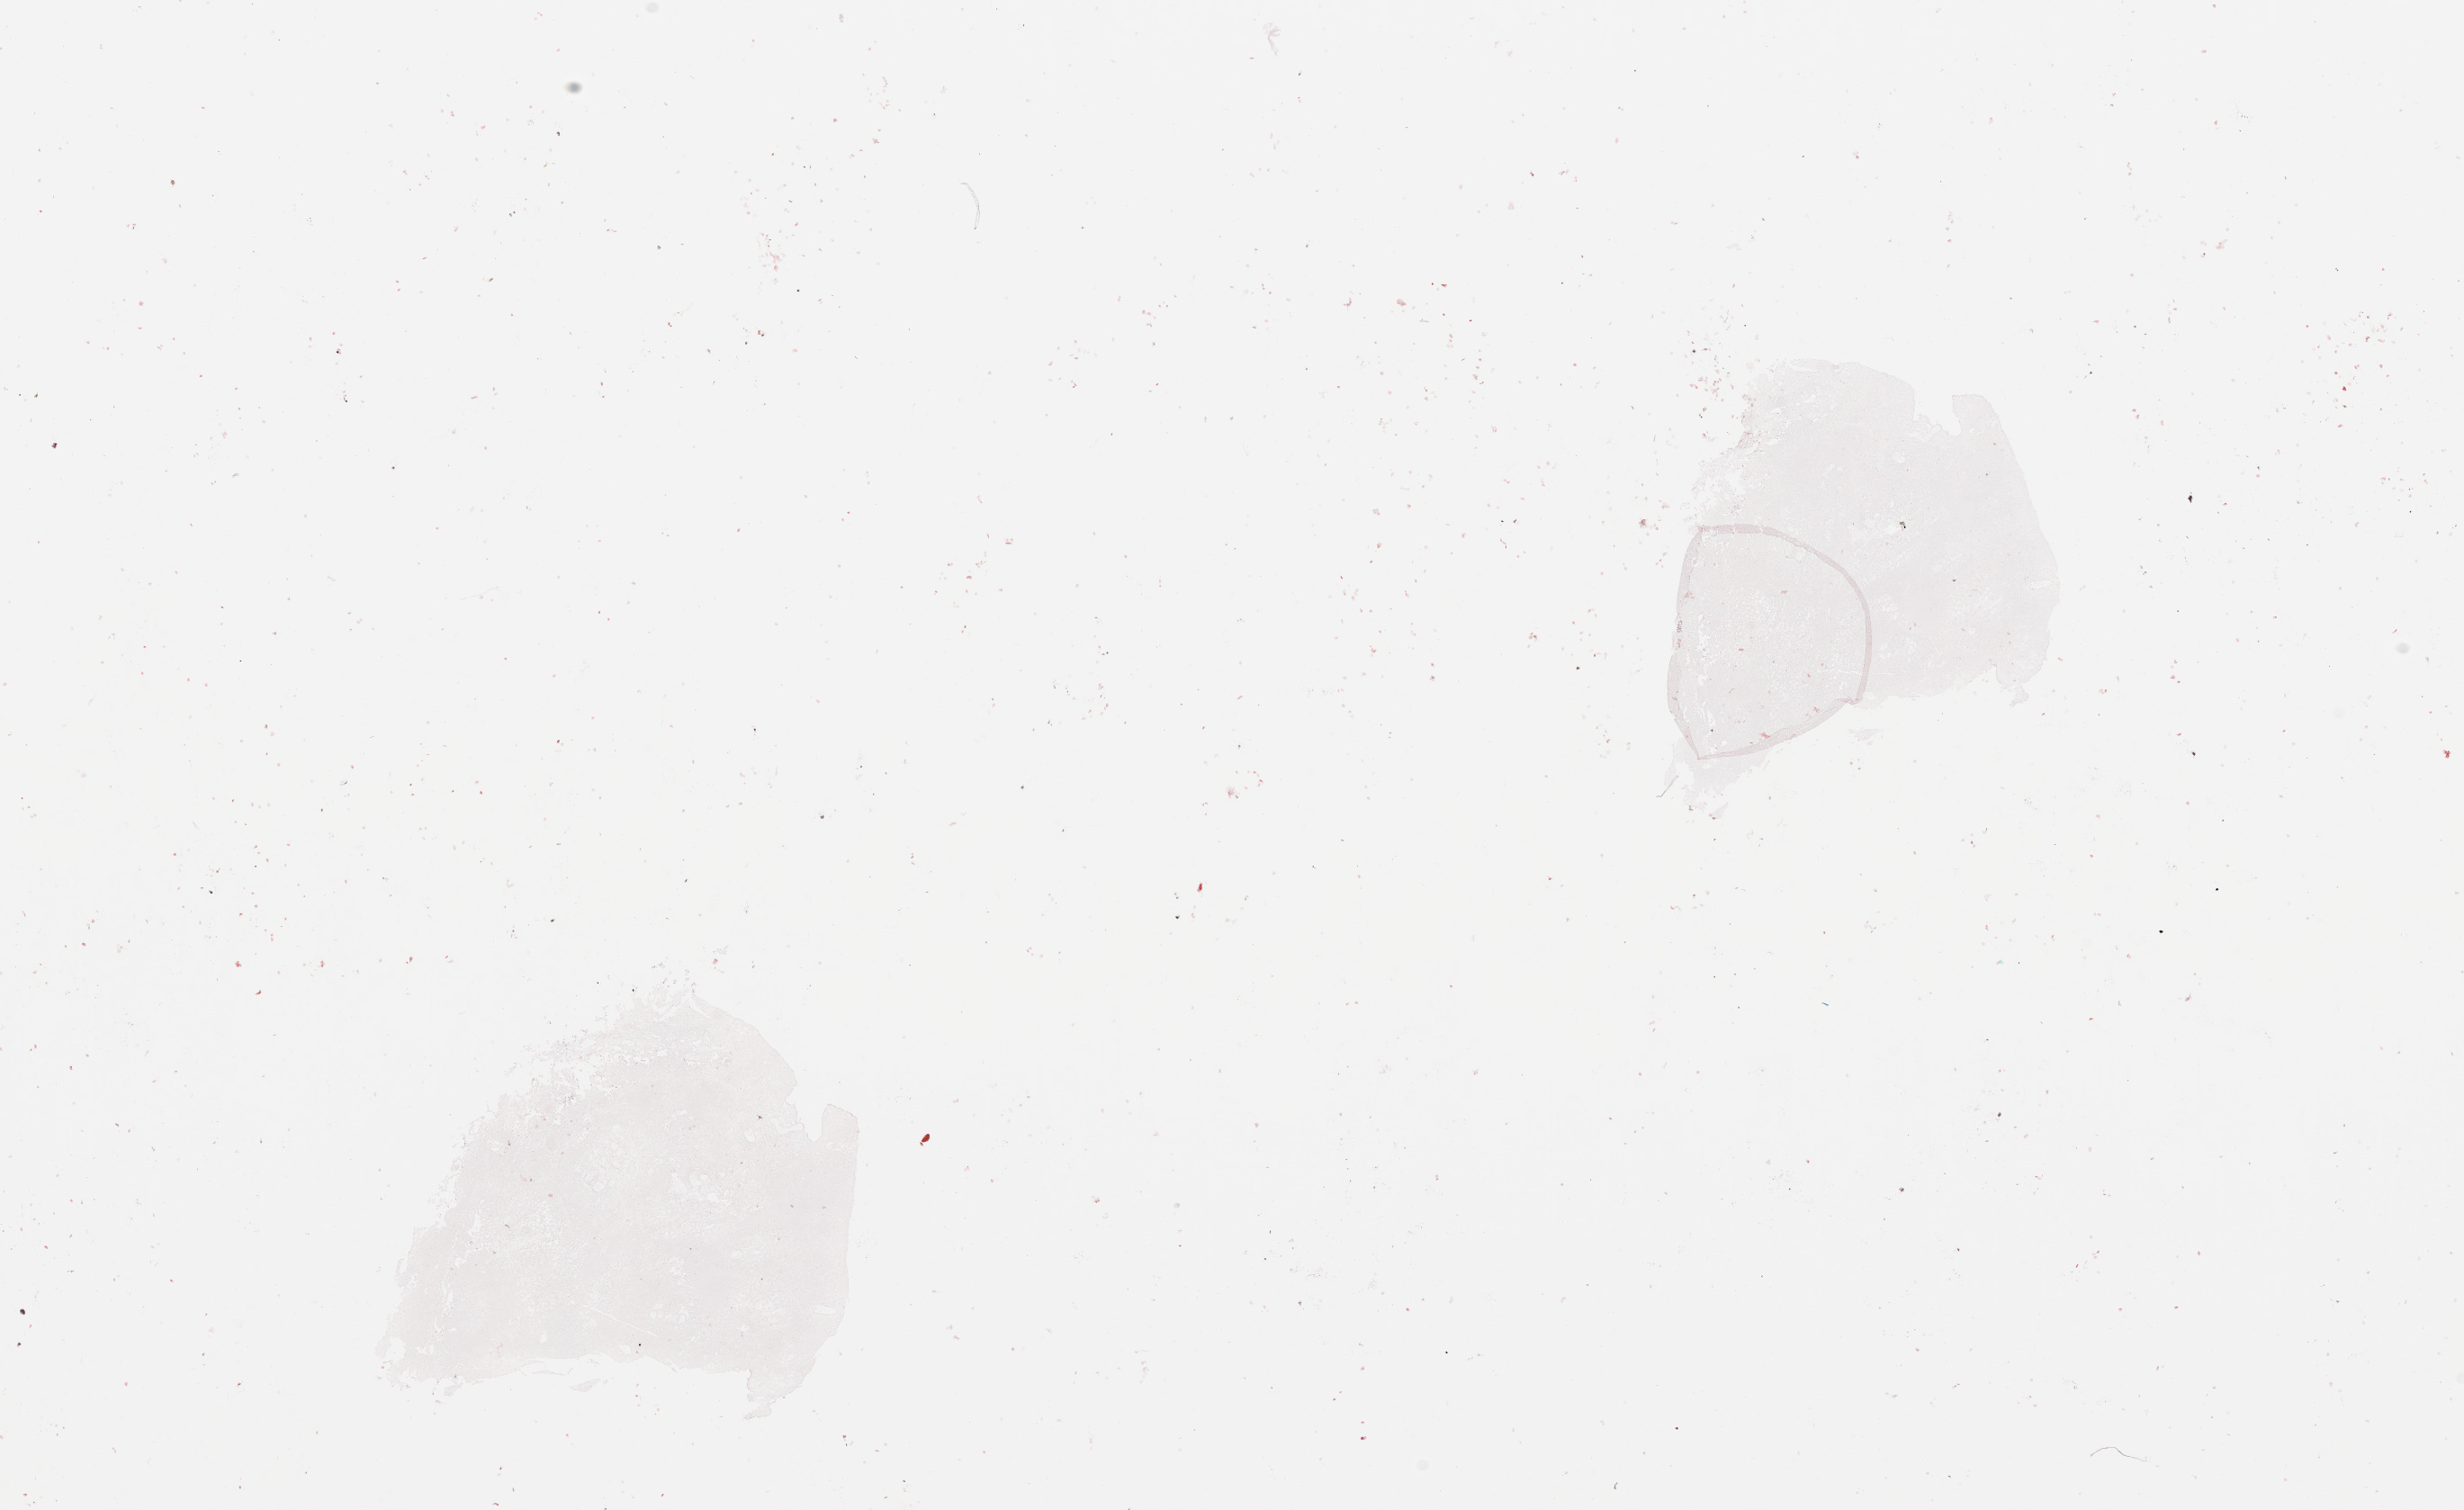
Hematoxylin and eosin (H&E) stained whole-slide image — low-resolution overview of the scanned area, about 21.7 x 13.3 mm (acquisition: 20x scan), tumour tissue sample, brain. Patient: male, age 59 years.
* primary tumour site (as recorded): frontal lobe
* diagnosis: Glioblastoma